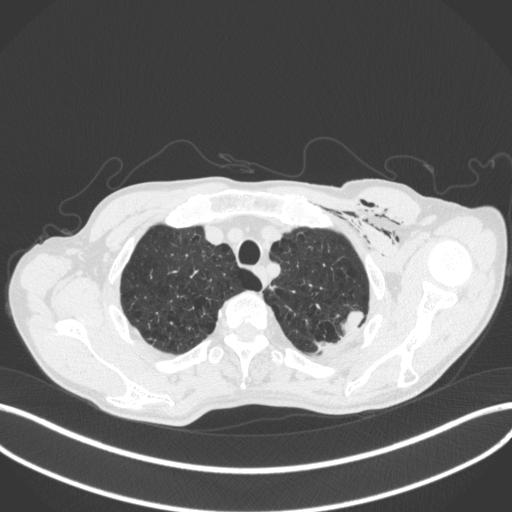
Chest CT, one axial slice. Position 355 of 416 along the scan axis. Reconstruction kernel B31f. Lung window (W 1500 / L -600 HU). 1 mm slice thickness. 512 × 512 image matrix. Male patient, age 58 years. From the clinical record (not read from this slice): clinical TNM (as recorded): T3 N0 M0.
Structures marked on this image (bounding box drawn by a radiologist):
- lung tumour (recorded histology: adenocarcinoma): bounding box (x1, y1, x2, y2) in pixels: (340, 308, 367, 336)